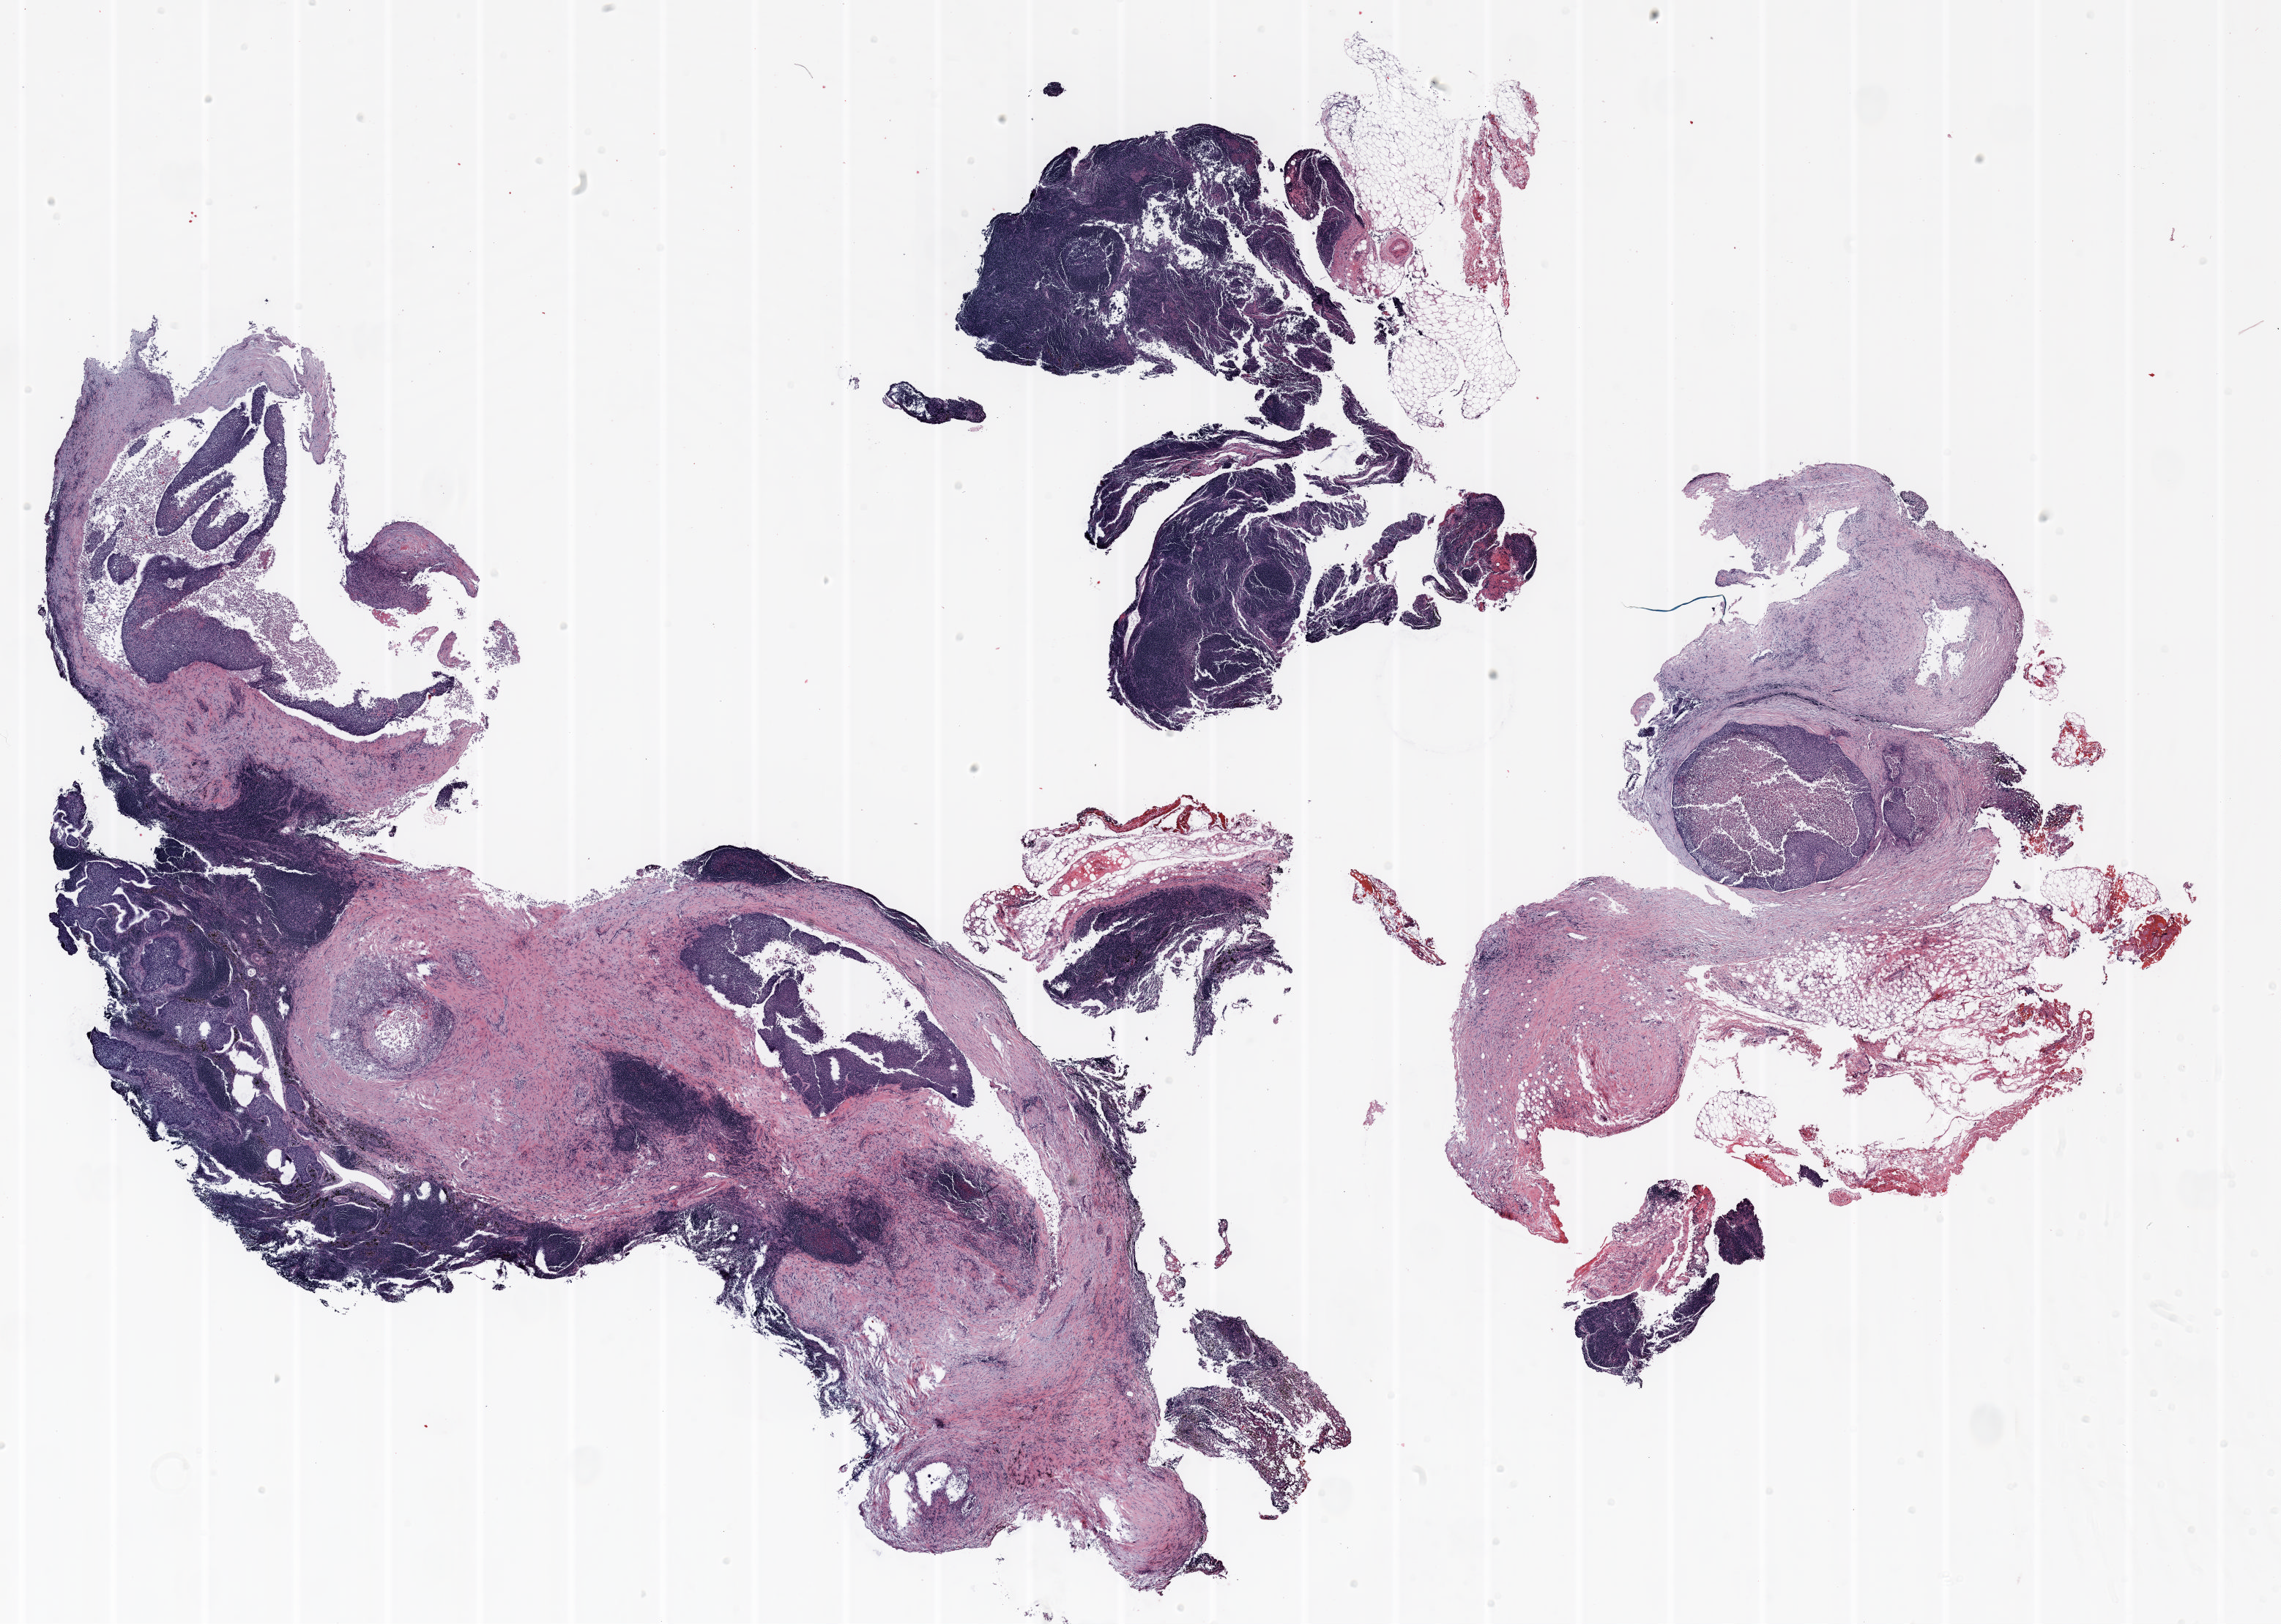
Whole-slide histology image, H&E-stained, low-resolution overview of the scanned area, about 25.0 x 17.8 mm (from a 20x scan); FFPE section; lung. Female, age 58 at enrolment. Former smoker at enrolment.
Participant's lung-cancer diagnosis: Squamous cell carcinoma, NOS.